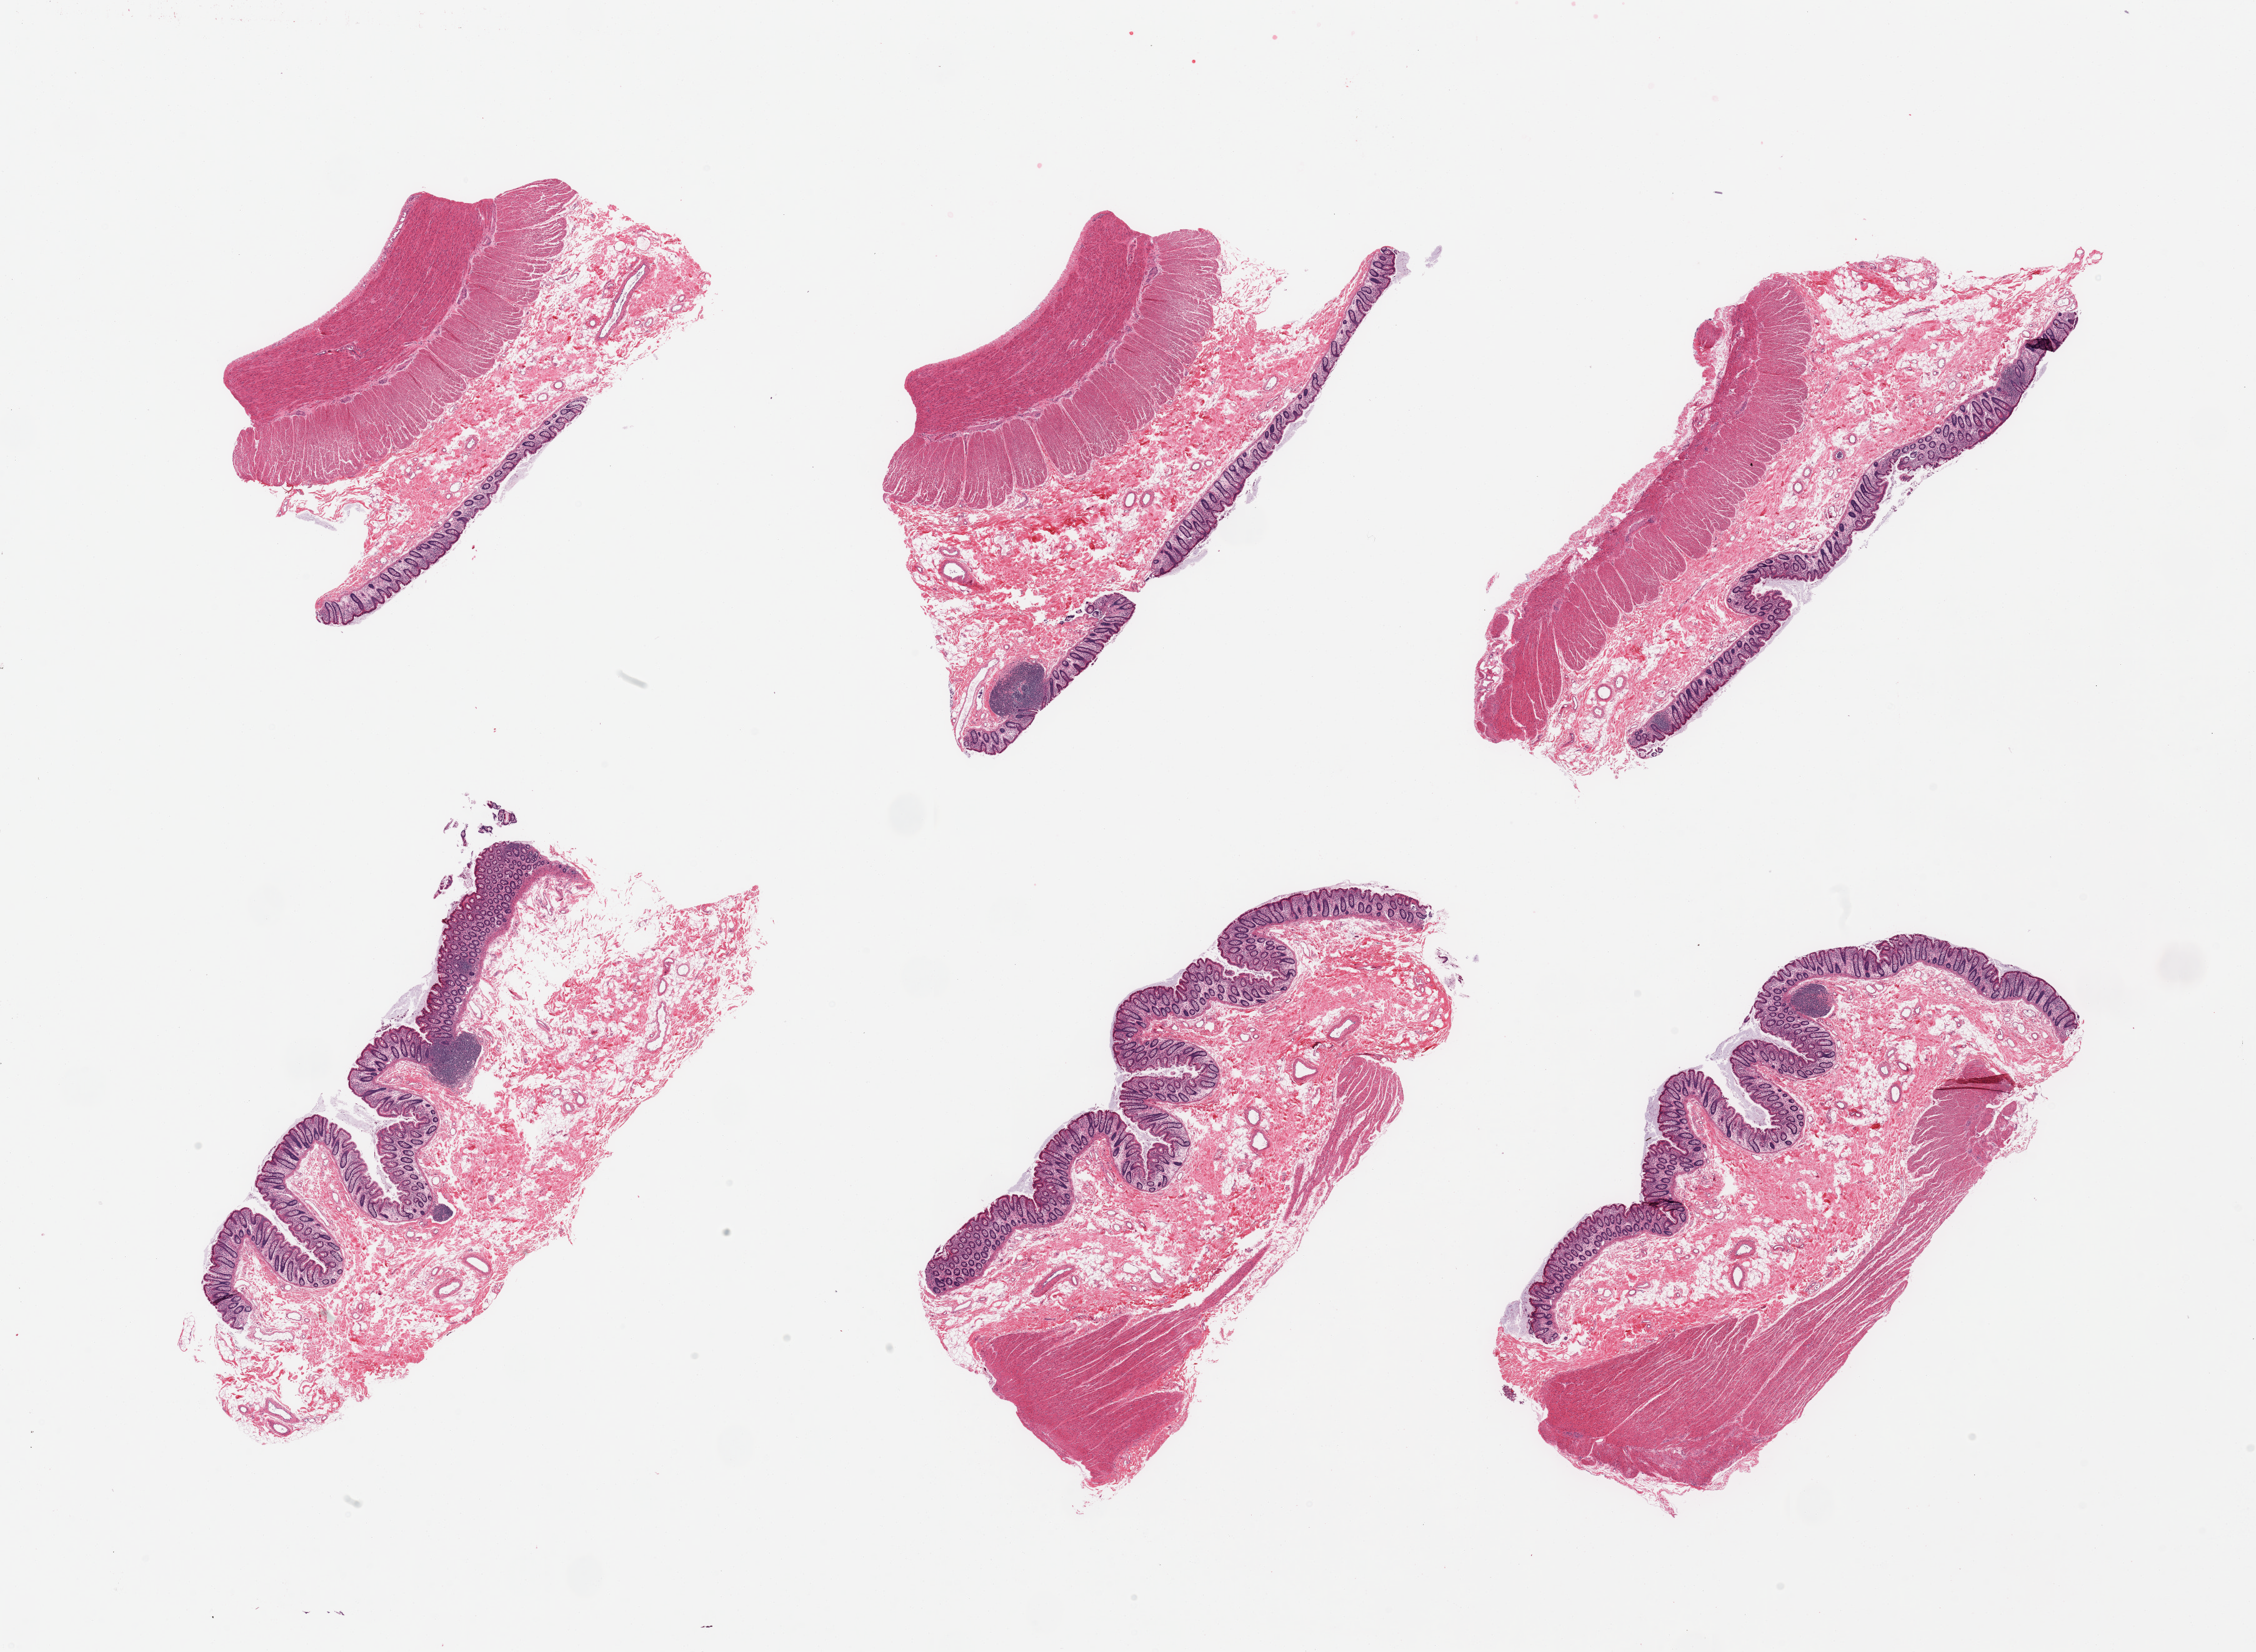
H&E whole-slide image, low-resolution overview of the scanned area, about 28.5 x 20.9 mm. PAXgene-fixed paraffin-embedded (PFPE) section. Sampled site (target tissue): transverse colon. Donor tissue sample. Donor: male.
• review note (as recorded): 6 pieces, mucosa well-preserved, ~0.5mm, ~15% thickness